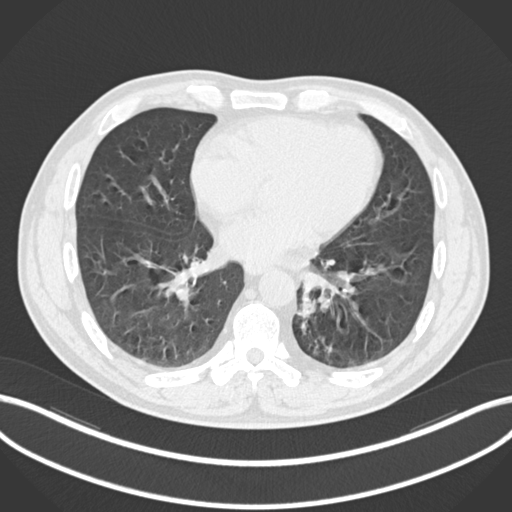
Chest CT, one axial slice; position 78 of 223 along the scan axis; reconstruction kernel B30f; 120 kVp; lung window (W 1500 / L -600 HU); 512 × 512 image matrix, field of view 400 × 400 mm. Patient: male, 50 years. From the clinical record (not read from this slice): clinical TNM (as recorded): T2a N3 M0.
Structures marked on this image (rectangle marked by the reading radiologist):
- lung tumour (recorded histology: squamous cell carcinoma): box from (x=295, y=287) to (x=316, y=319) px